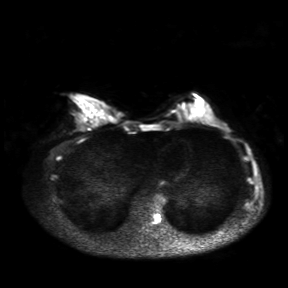
Breast MRI, one axial slice. Slice 13 of 30 in the series (ordered by position). Diffusion-weighted series; image 2 of 4 stored at this slice position (different b-values; order by instance number). 3 T. 288 × 288 image matrix, field of view 360 × 360 mm. Female patient.
Structures marked on this image (expert manual segmentation):
- tumour on diffusion-weighted imaging: box from (x=175, y=107) to (x=186, y=116) px